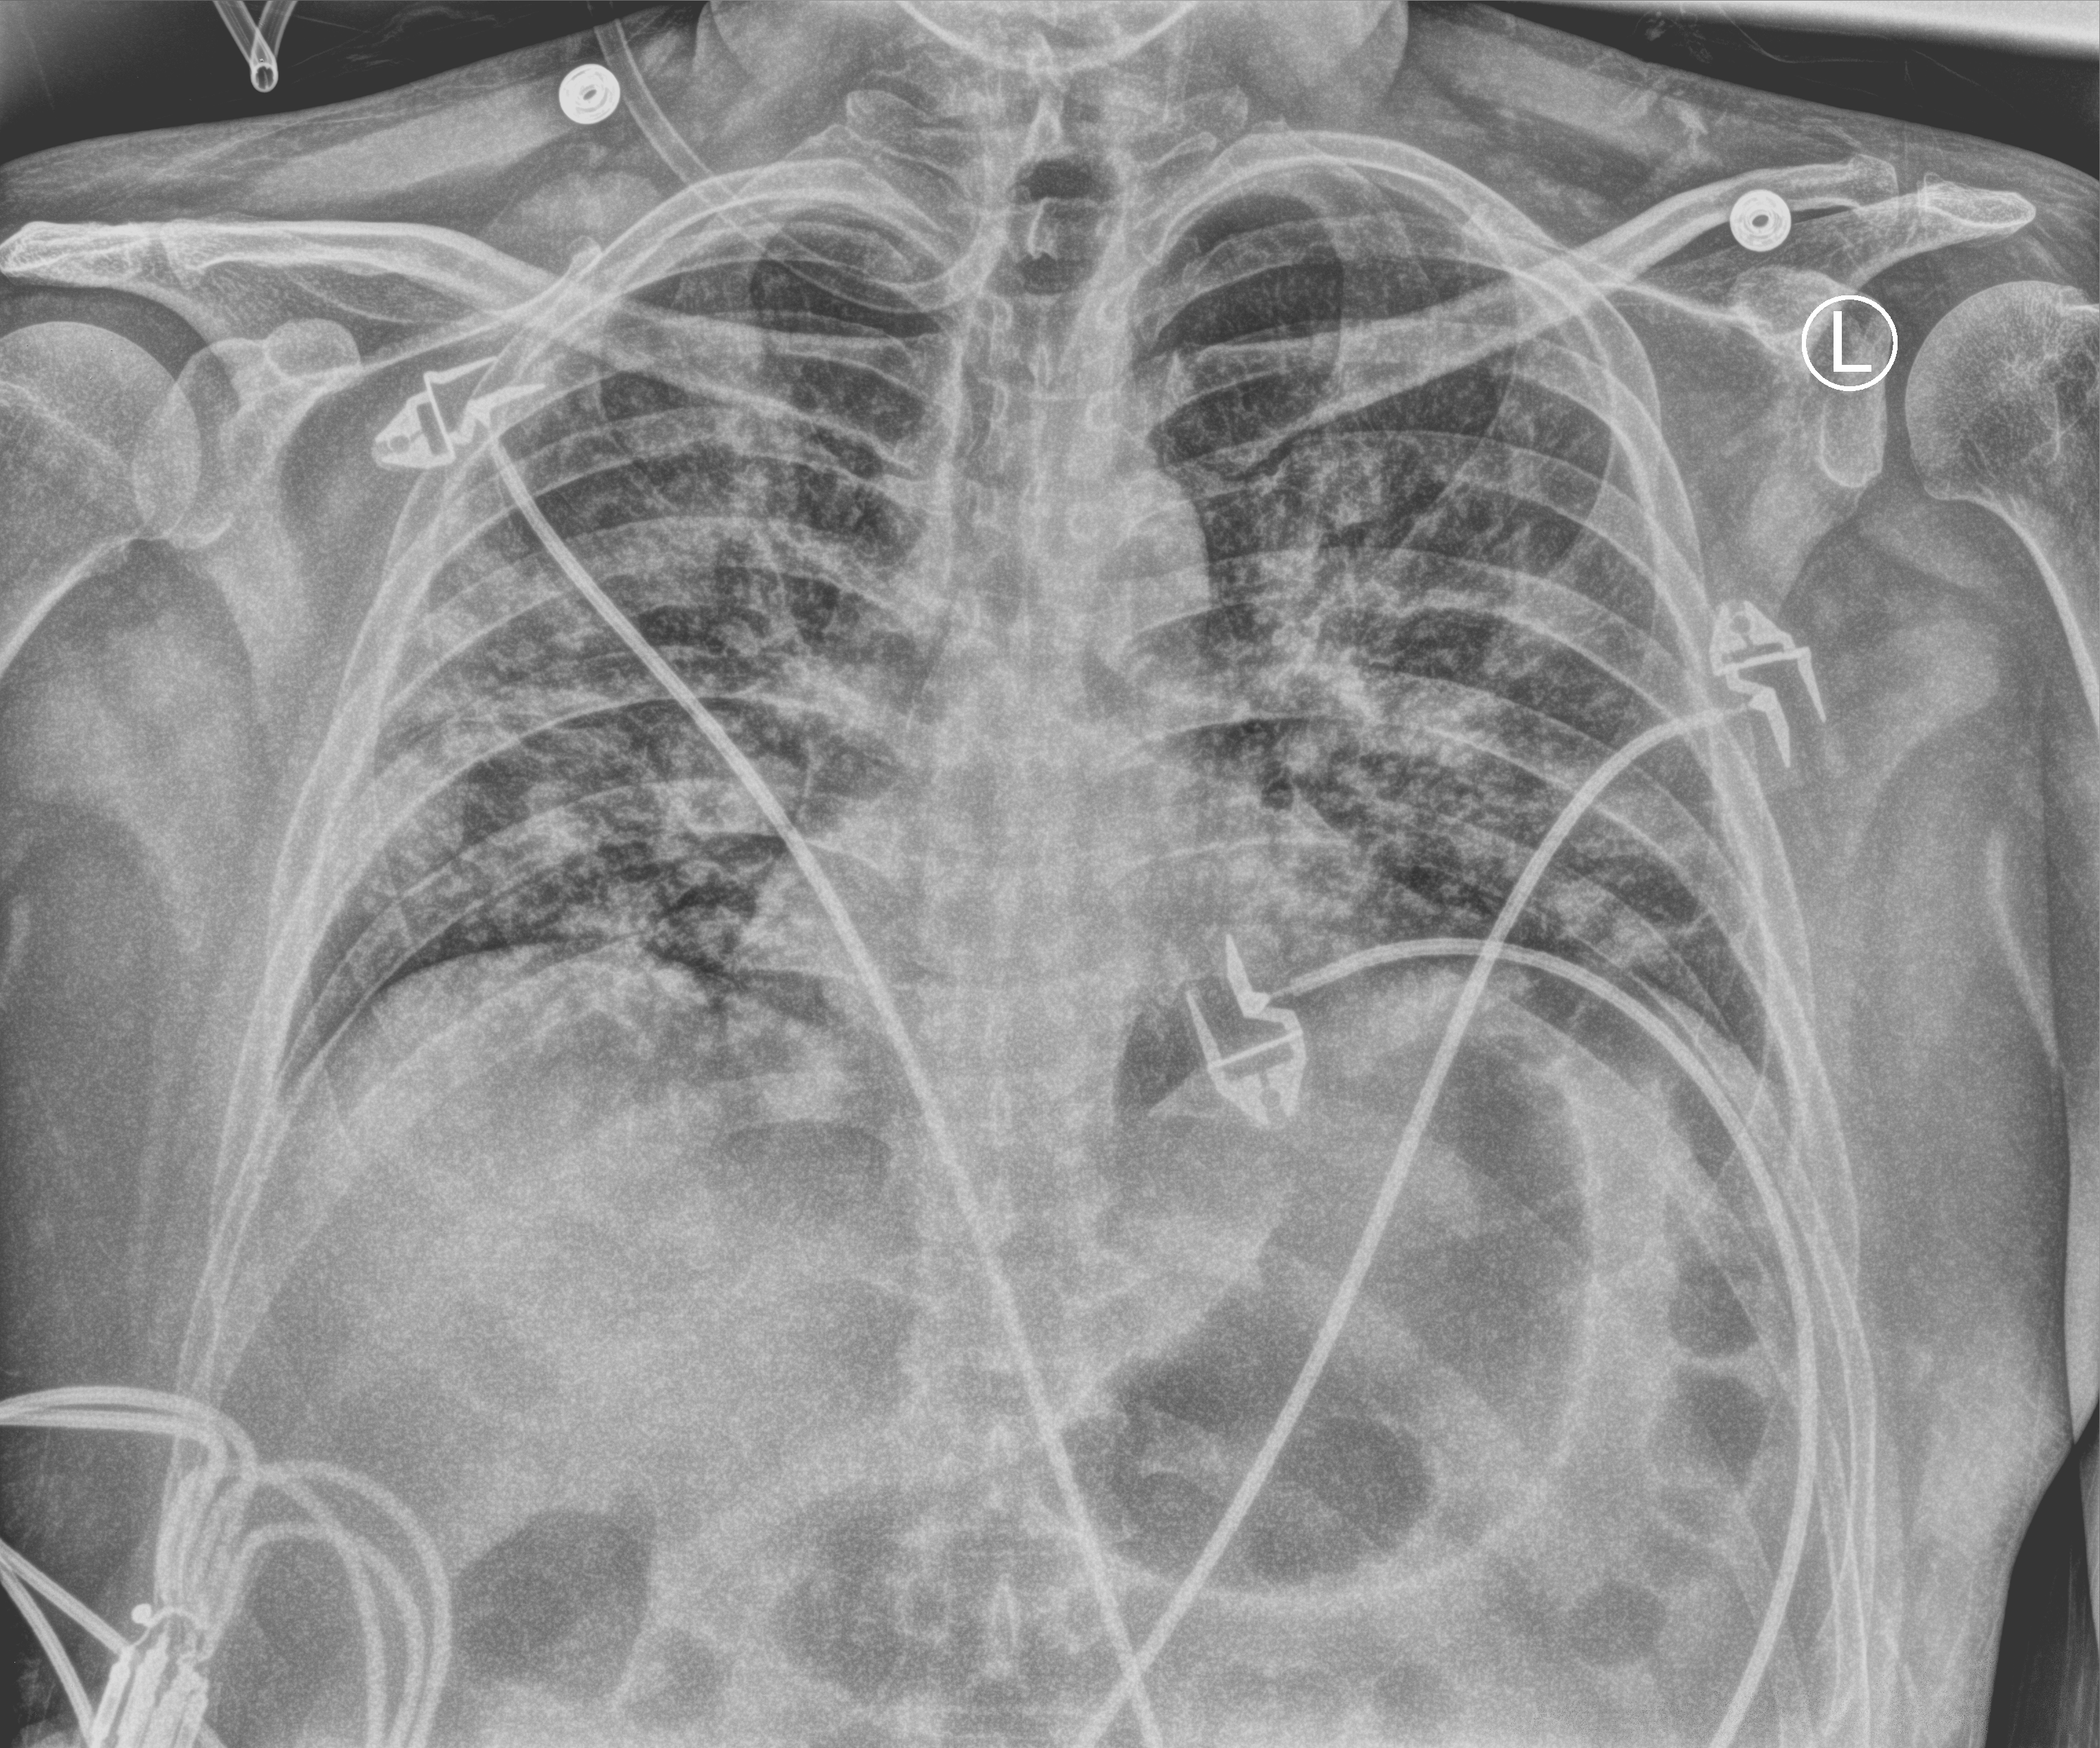
Portable chest radiograph; anteroposterior (AP) projection. Male patient hospitalised with COVID-19, age 18–59 years.
From the hospital-stay record, not from the radiograph (when in the stay this image was taken is not recorded): other chronic lung disease (admission record): no; COPD (admission record): no; mechanically ventilated during this hospital stay: no.